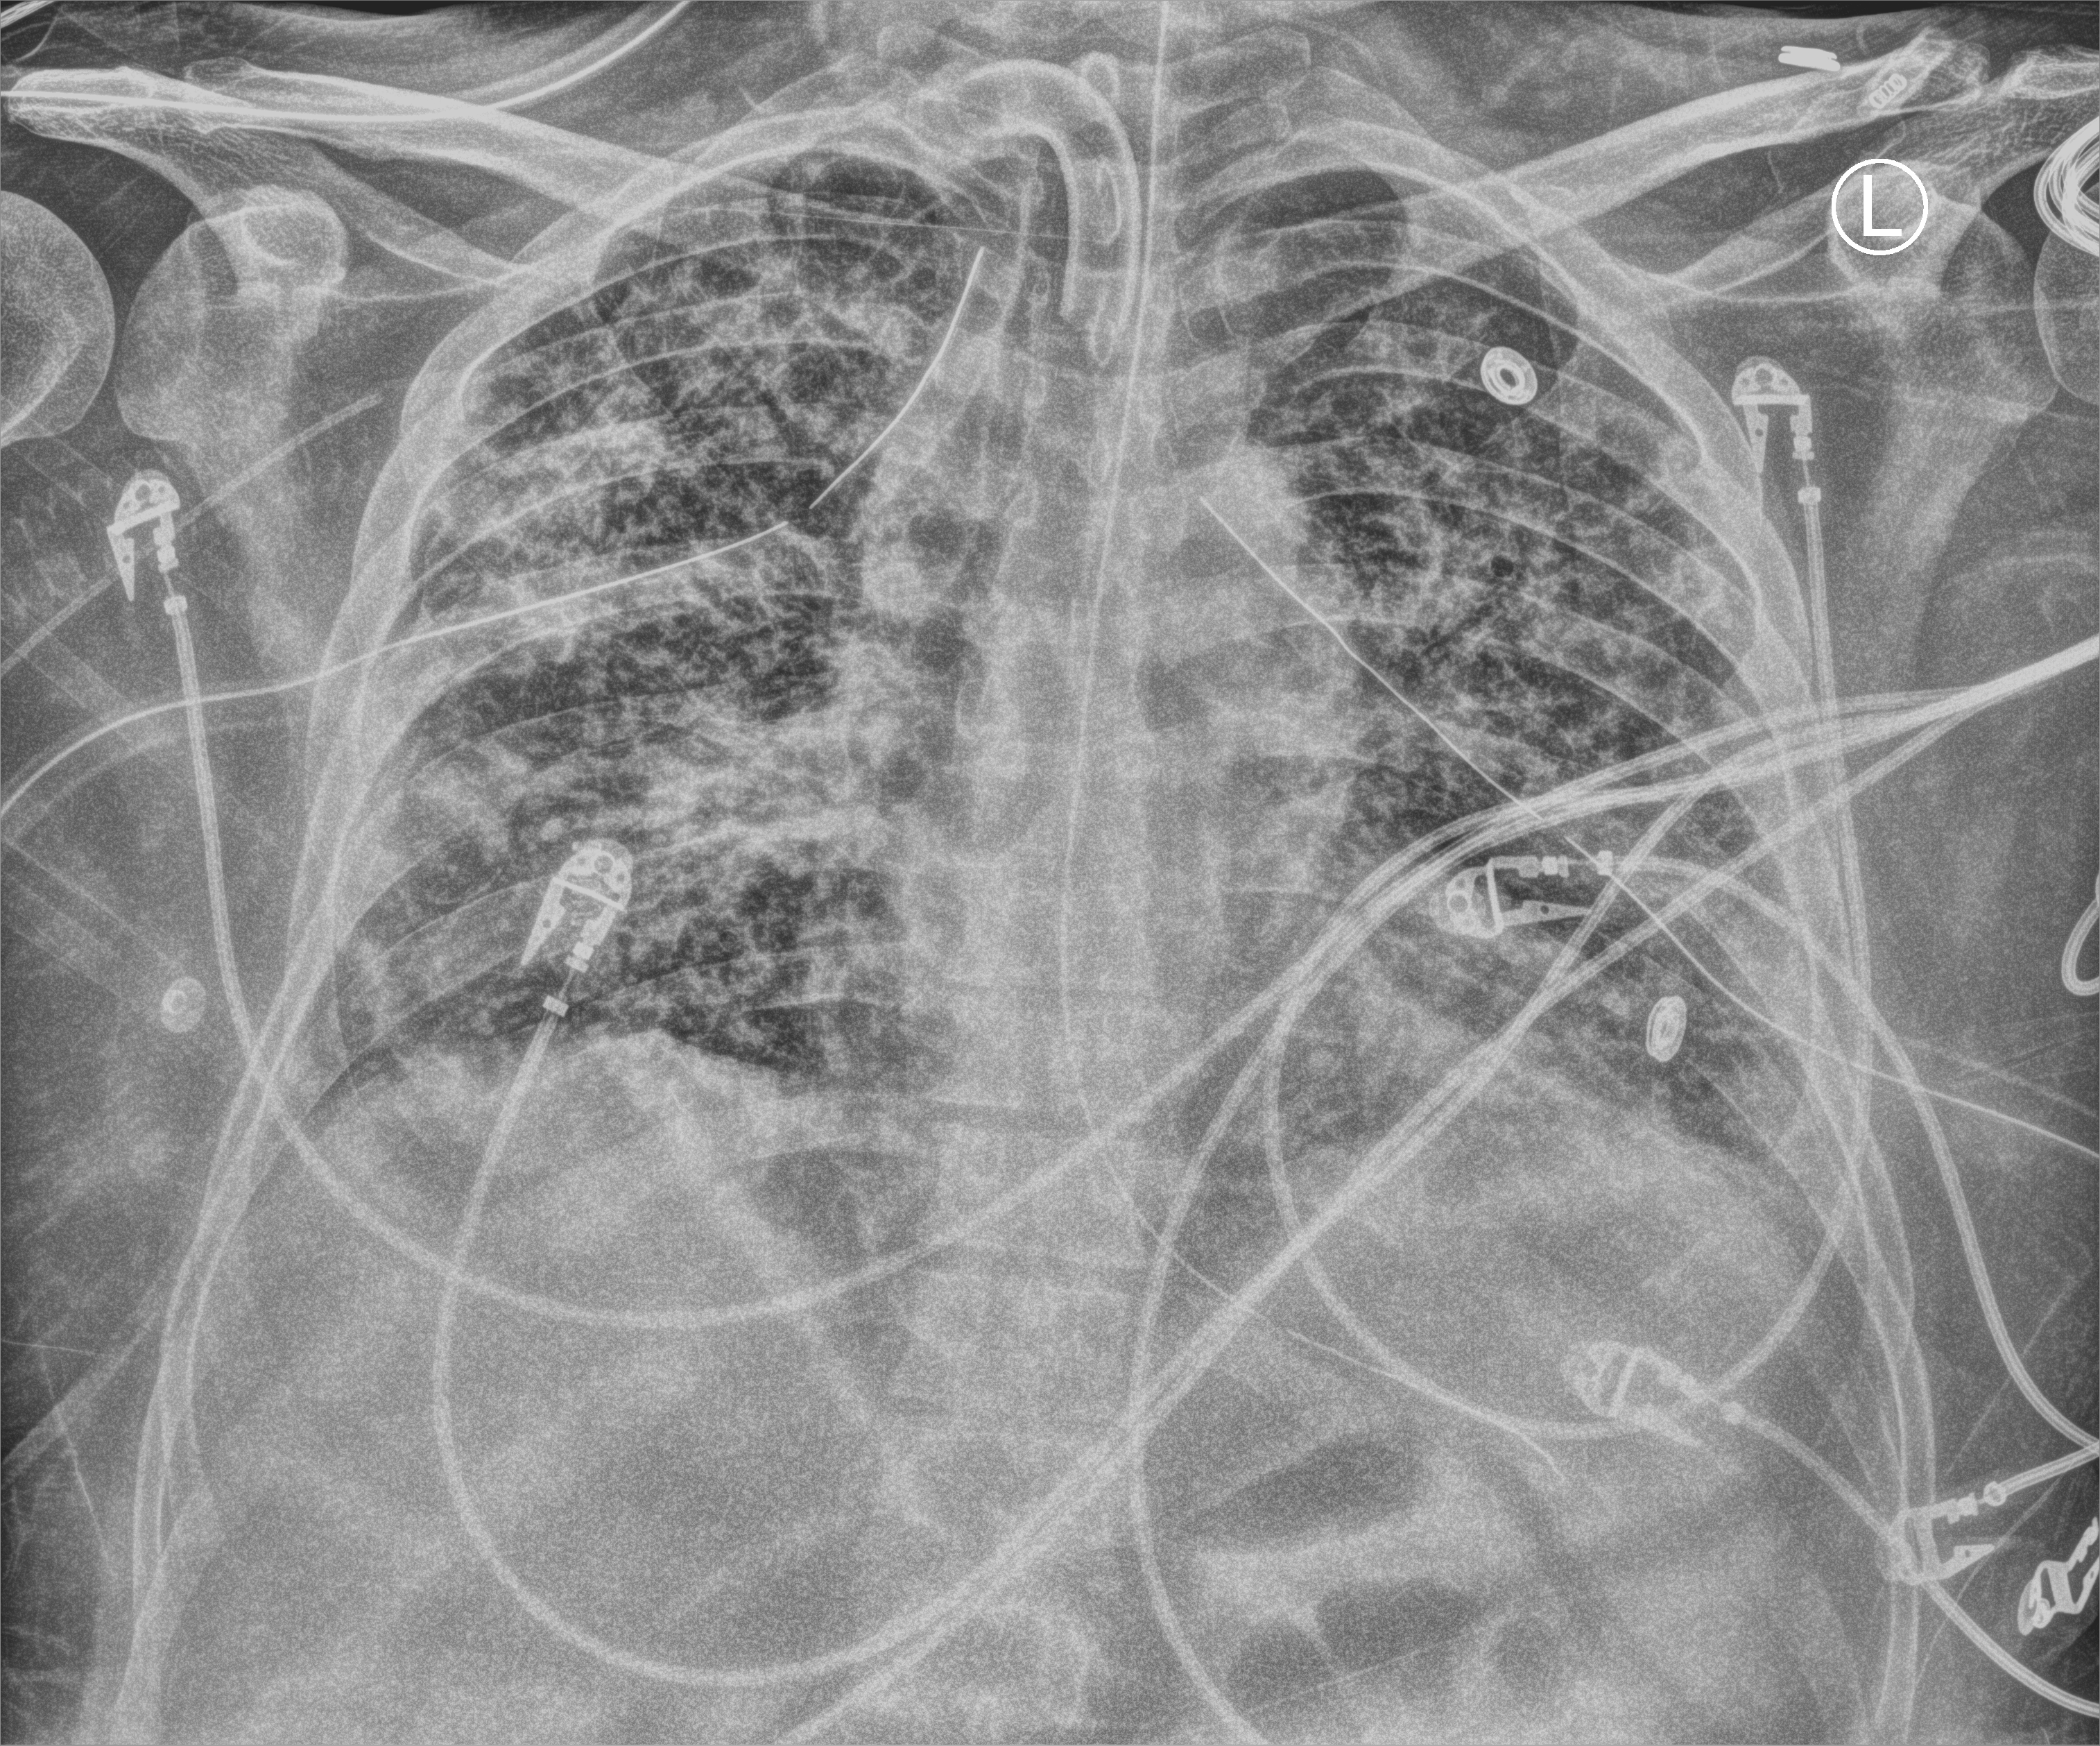
Bedside chest radiograph (computed radiography); anteroposterior (AP) projection. Male patient hospitalised with COVID-19, age 18–59 years.
Hospital-stay facts (about this admission, not read from this image; timing relative to this image not recorded): mechanically ventilated during this hospital stay: yes; length of hospital stay: 63 days.